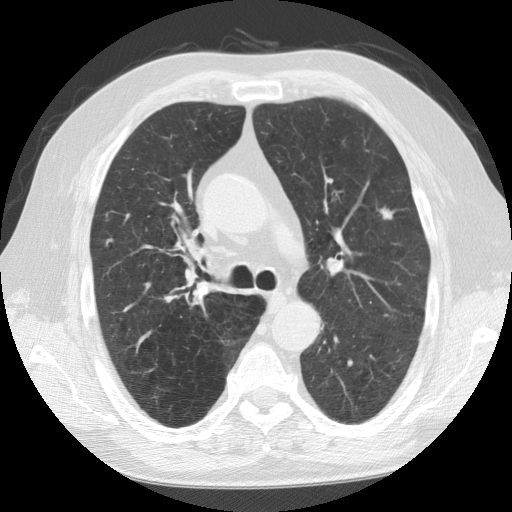
Low-dose screening chest CT, axial slice. Second screening round (one year after baseline). Lung window (W 1500 / L -600 HU). Slice 43 of 109 in the series. Male, age 64 years at enrolment.
- Expert-annotated lung lesion, bounding box (x1, y1, x2, y2) in pixels: (371, 201, 407, 231).
- The screening reader recorded 2 non-calcified nodules or masses ≥4 mm on this exam (left upper lobe, right lower lobe); which of them this box marks is not recorded.
- Later outcome: lung cancer diagnosed 233 days after this screen — squamous cell carcinoma, NOS, left upper lobe, moderately differentiated (G2), stage IA (AJCC 6th edition), 10 mm at pathology.